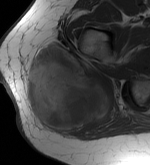
MRI of an extremity soft-tissue mass, one axial slice. Slice 24 of 56 in the series (ordered by position). MR volume resampled by the dataset authors to the PET/CT grid (not the native acquisition matrix). 150 × 165 image matrix, field of view 146 × 161 mm. Female patient. From the clinical record (not read from this slice): histological type: epithelioid sarcoma with vascular differentiation; site of the primary tumour: right buttock.
Outlined on this slice (expert contour drawn on MRI and transferred to this co-registered scan by the dataset authors):
- gross tumour volume (mass): bounding box [x1, y1, x2, y2] px = [25, 41, 113, 137]